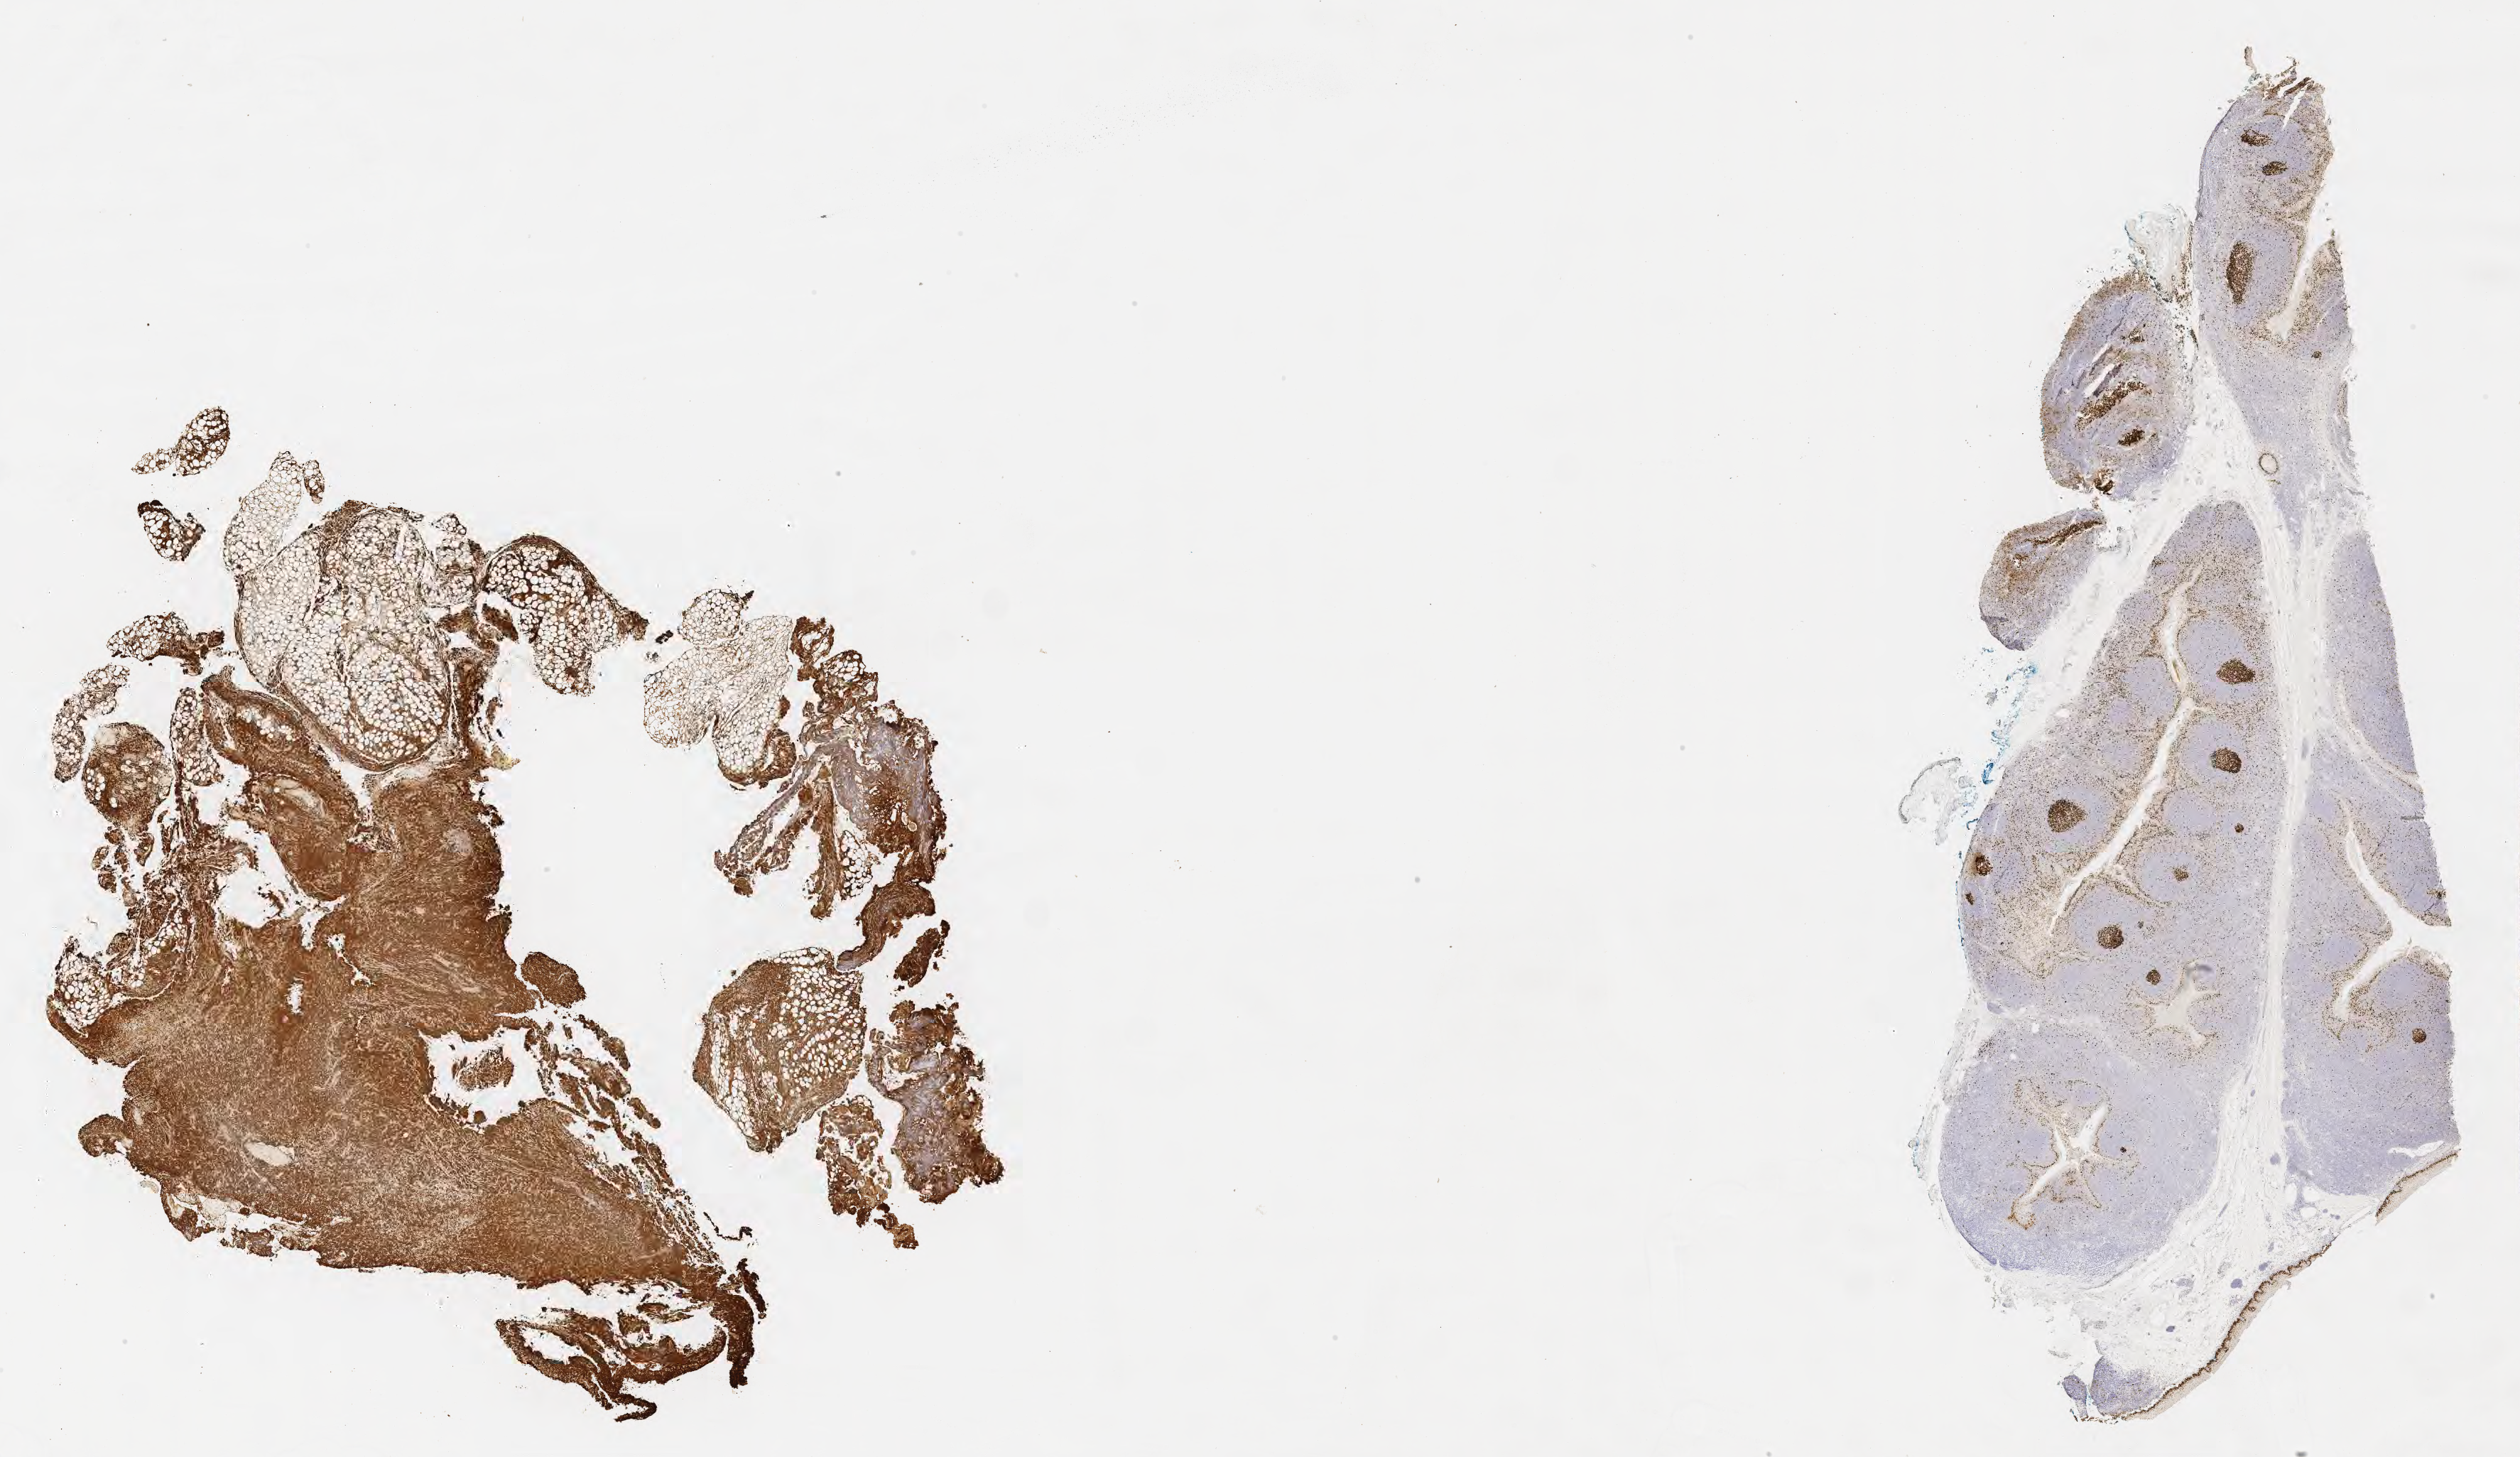
IHC for Ki-67, whole-slide image — whole scanned area (about 28.7 x 16.6 mm) shown as a low-resolution overview; specimen: tumor tissue; anatomic site: abdominal lymph node. Patient: male, age at initial diagnosis 9 years.
Diagnosis: Burkitt lymphoma, NOS.